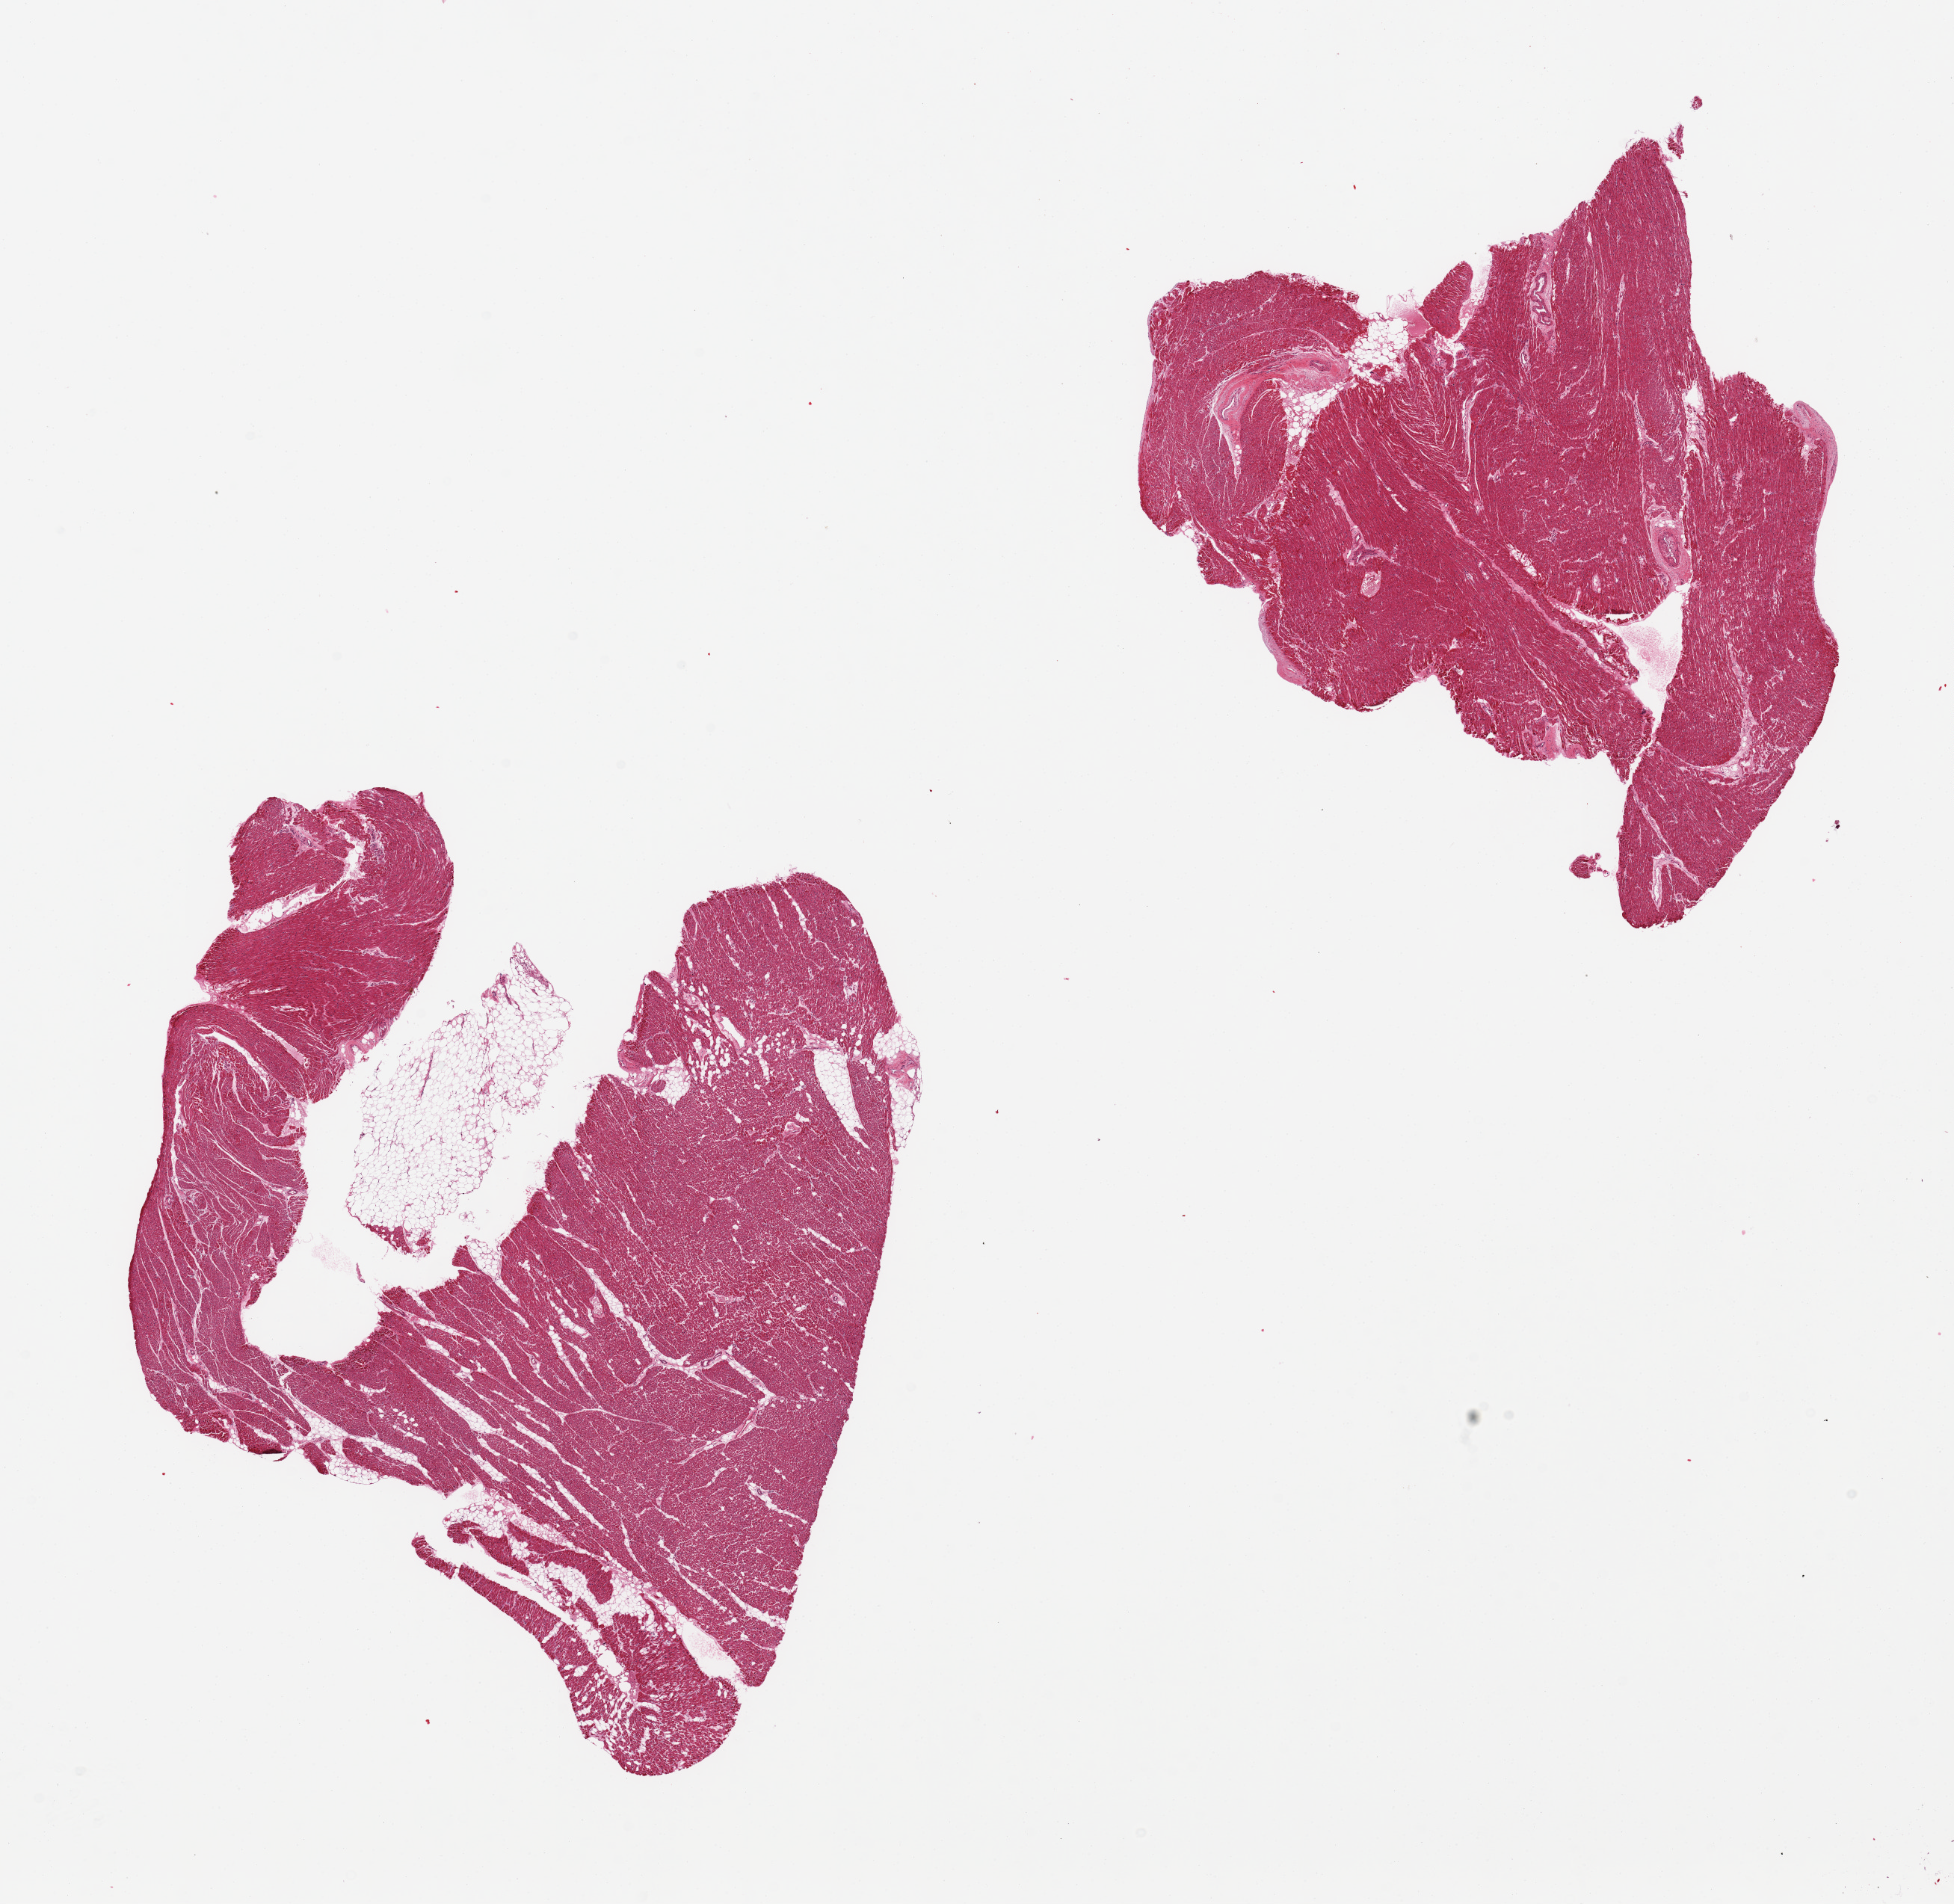
Haematoxylin and eosin whole-slide image, brightfield — whole scanned area (about 20.7 x 20.1 mm) shown as a low-resolution overview, PAXgene-fixed, paraffin-embedded tissue, sampled site (target tissue): heart, donor tissue sample.
* review note (as recorded): 2 pieces, minimal ischemic damage